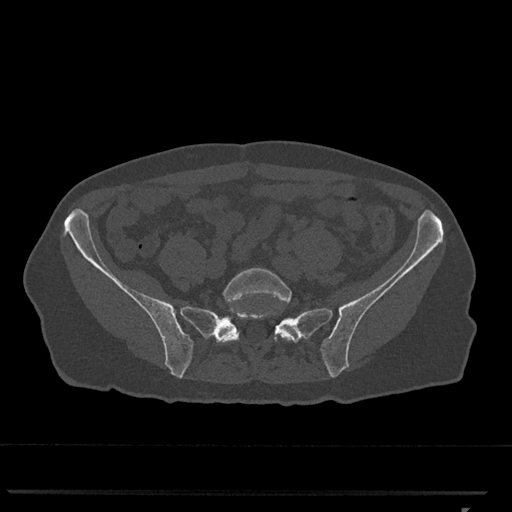
CT including the spine, one axial slice; position 122 of 793 along the scan axis; bone window (W 1800 / L 400 HU); 0.5 mm slice thickness; 512 × 512 image matrix. Patient: female, 62 years. Case-level facts recorded for this patient, not image findings: primary cancer: renal.
Outlined on this slice (semi-automatic segmentation, software-assisted and operator-edited):
- L5 vertebra: bounding box (x1, y1, x2, y2) in pixels: (219, 268, 297, 342)